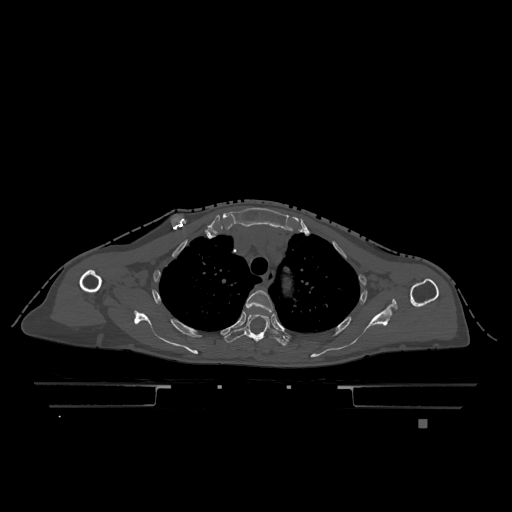
CT including the spine, one axial slice. Slice 896 of 1317 in the series (ordered by position). Bone window (W 1800 / L 400 HU). 0.5 mm slice thickness. 512 × 512 image matrix, field of view 500 × 500 mm. Patient: female, 74 years. Case-level facts recorded for this patient, not image findings: primary cancer: lung.
Outlined on this slice (semi-automatic segmentation, software-assisted and operator-edited):
- T3 vertebra: box from (x=246, y=290) to (x=273, y=312) px
- T4 vertebra: (x=224, y=313)–(x=290, y=346)